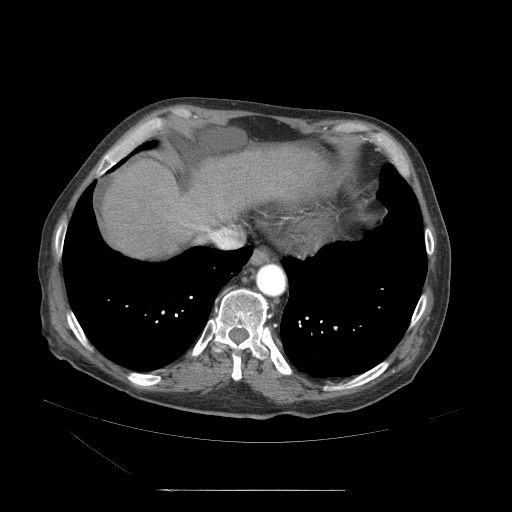
Contrast-enhanced abdominal CT (liver protocol), one axial slice; position 53 of 71 along the scan axis; reconstruction kernel STANDARD; soft-tissue window (W 400 / L 40 HU); 2.5 mm slice thickness; 512 × 512 image matrix. Case-level facts recorded for this patient, not image findings: diagnosis: hepatocellular carcinoma (patient treated with transarterial chemoembolisation; whether this scan precedes or follows treatment is not stated here); TNM stage (as recorded): Stage-II; Child-Pugh class: A.
Outlined on this slice (semi-automatic segmentation, software-assisted and operator-edited):
- abdominal aorta: box from (x=256, y=265) to (x=286, y=297) px
- liver parenchyma outside the tumour (the mass and vessels are separate outlines, so this box may not span the whole liver): (x=116, y=146)–(x=317, y=260)
- liver vessels: (x=118, y=197)–(x=249, y=252)